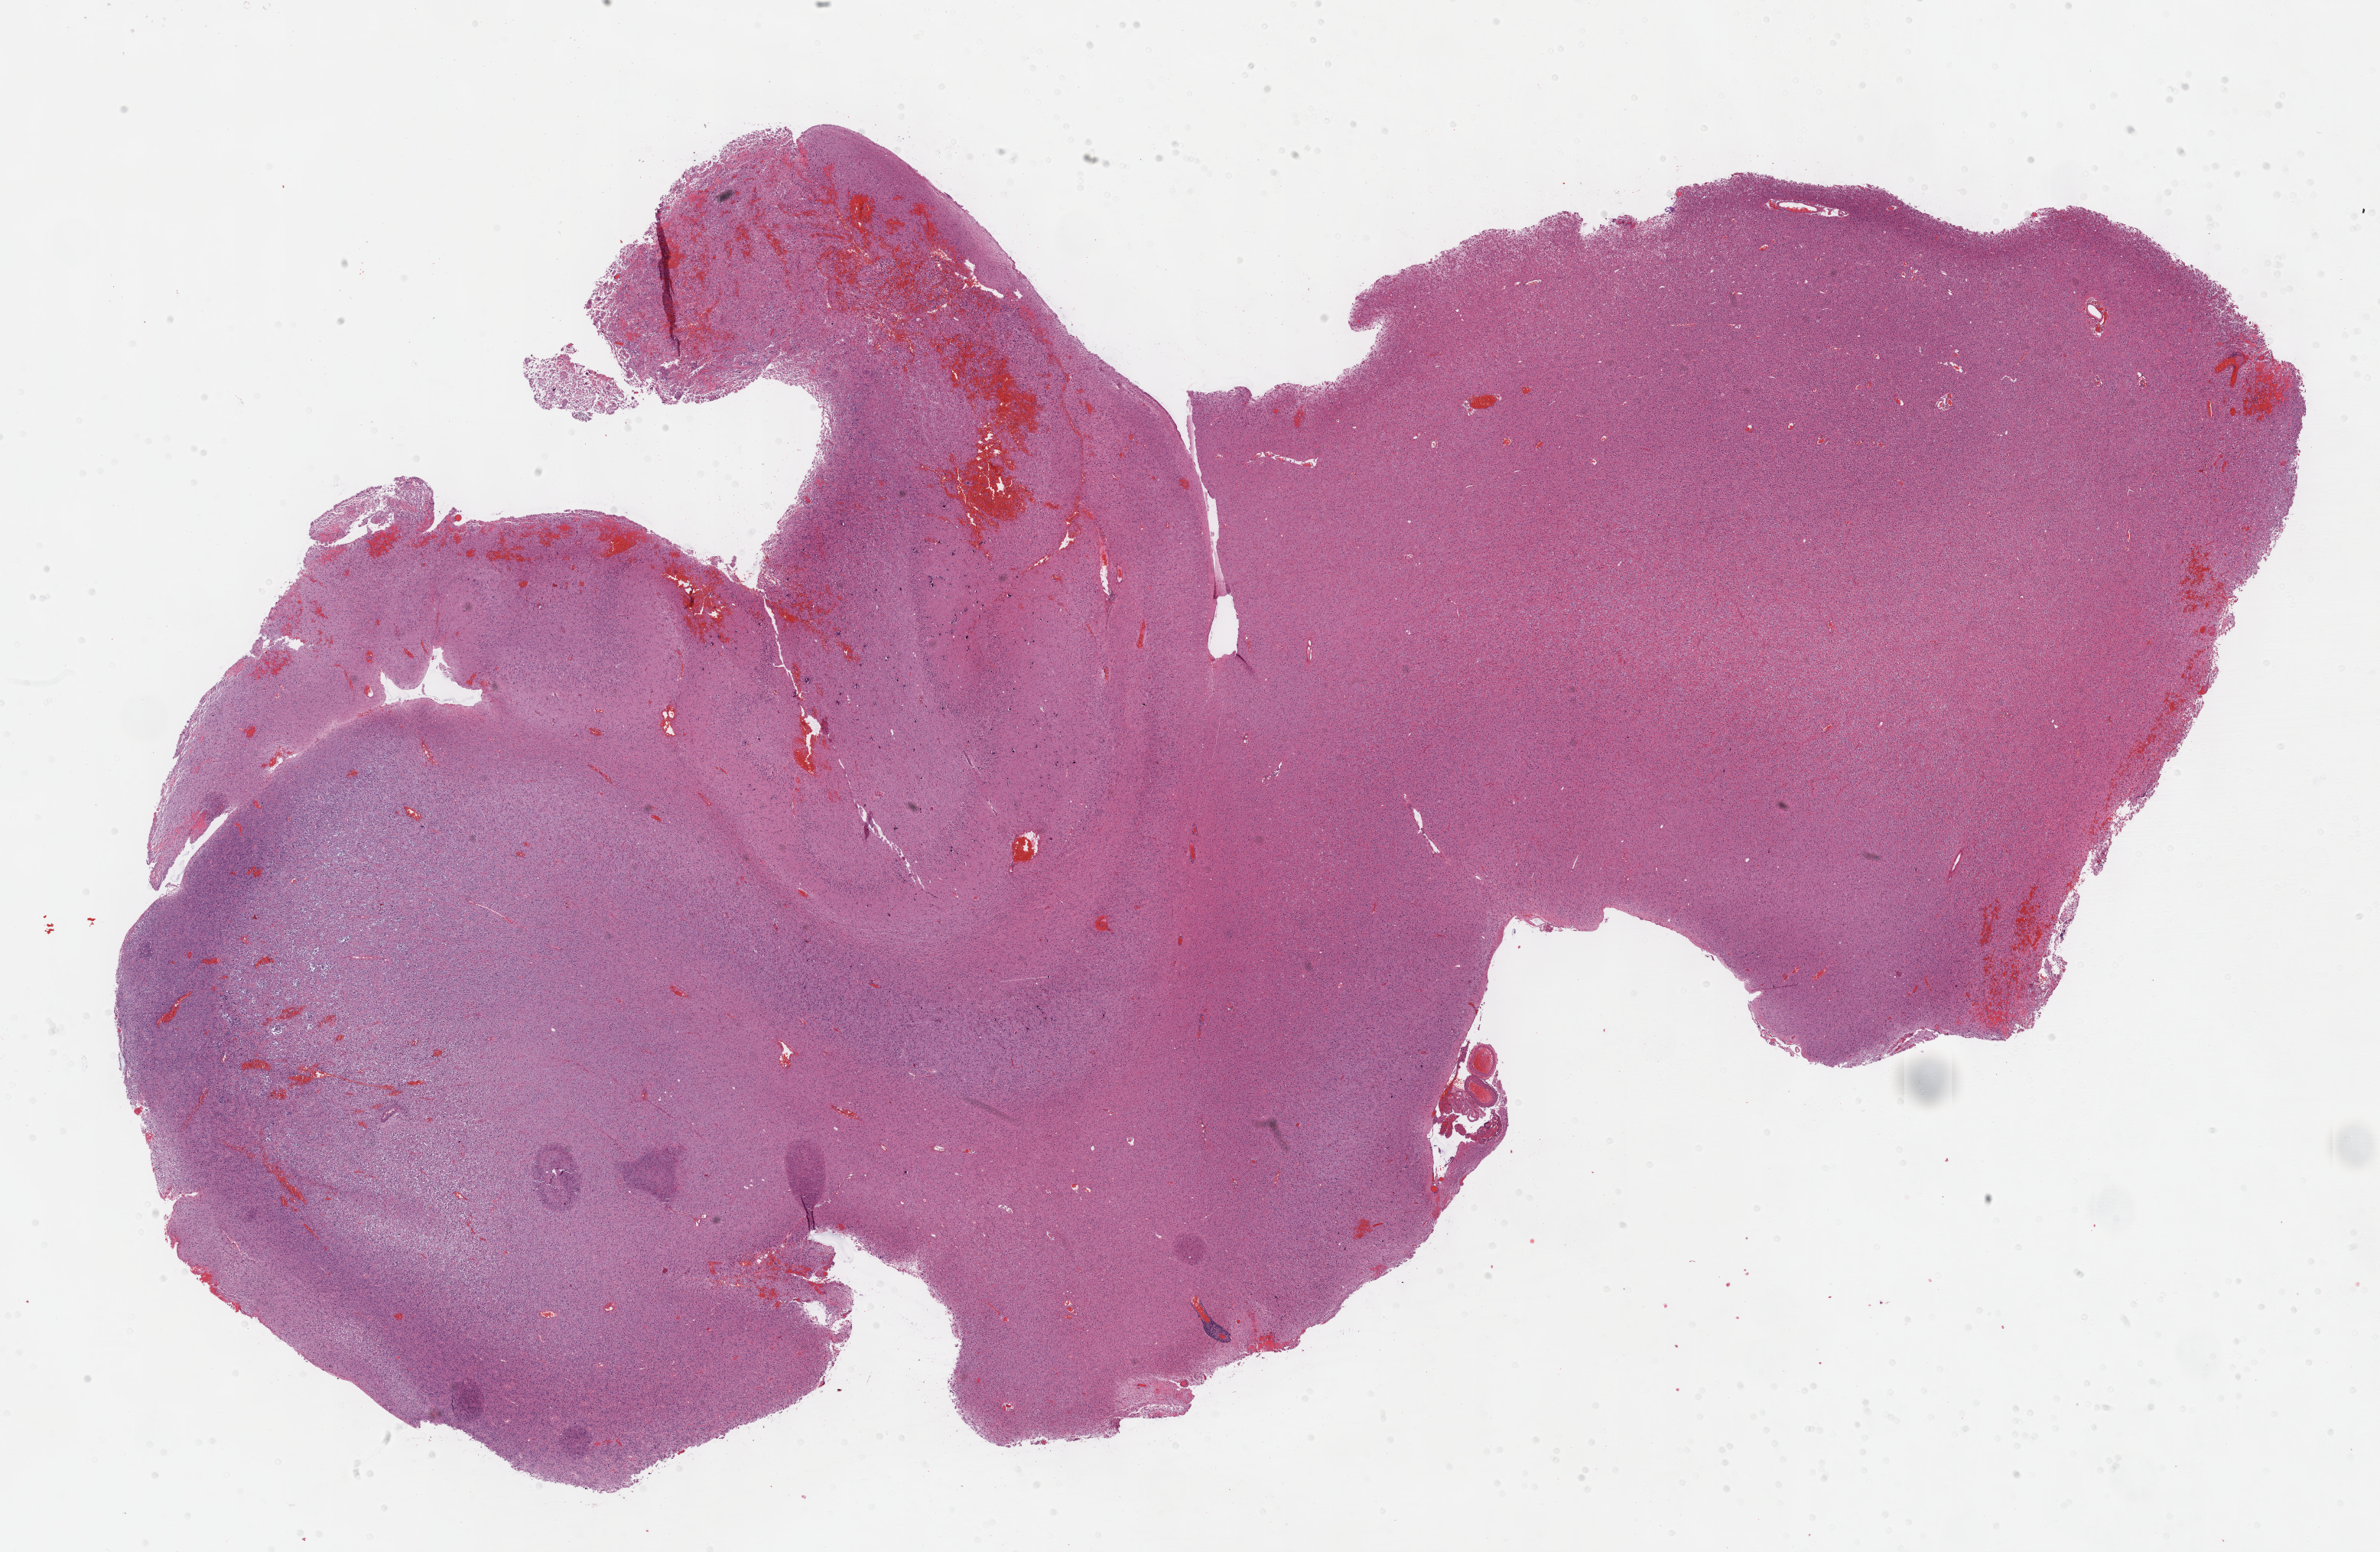
Whole-slide histology image, Hematoxylin and eosin (H&E) stained — whole scanned area (about 25.2 x 16.4 mm, slide scanned at 40x) shown as a low-resolution overview; FFPE section; sample: primary tumour, brain. Patient: male, age at initial diagnosis 37 years. Histologic grade: G3 (poorly differentiated).
Pathologic diagnosis: Oligodendroglioma, anaplastic. Laterality: right.